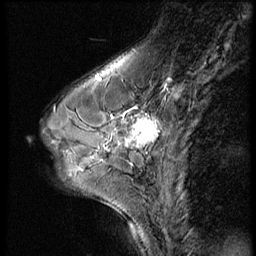
Breast MRI (dynamic contrast-enhanced), one sagittal slice. Position 20 of 56 along the scan axis. Dynamic contrast-enhanced series, image 2 of 3 at this slice position (ordered by acquisition). 1.5 T. TE 4.2 ms, TR 9 ms. 256 × 256 image matrix. Patient: female, 46 years. From the clinical record (not read from this slice): setting: breast cancer imaged before/during neoadjuvant chemotherapy; receptor status: HER2-positive.
Annotated regions visible in this slice (semi-automatic segmentation, software-assisted and operator-edited):
- analysis volume of interest (the breast-tissue region the enhancement analysis was run in; not a lesion): bounding box (x1, y1, x2, y2) in pixels: (64, 98, 174, 182)
- tumour enhancement mask (voxels above the 140 % enhancement threshold inside the analysis volume of interest): (120, 117, 159, 149)